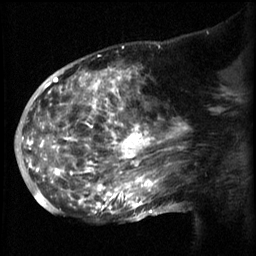
Breast MRI (dynamic contrast-enhanced), one sagittal slice; slice 34 of 60 in the series (ordered by position); 3 images stored at this slice position (order not interpretable as contrast timing); 1.5 T; TE 4.2 ms, TR 8.2 ms; 256 × 256 image matrix. Patient: female, 50 years.
Outlined on this slice (semi-automatic segmentation, software-assisted and operator-edited):
- analysis volume of interest (the breast-tissue region the enhancement analysis was run in; not a lesion): box from (x=50, y=64) to (x=169, y=217) px
- tumour enhancement mask (voxels above the 70 % enhancement threshold inside the analysis volume of interest): (x=50, y=64)–(x=169, y=215)